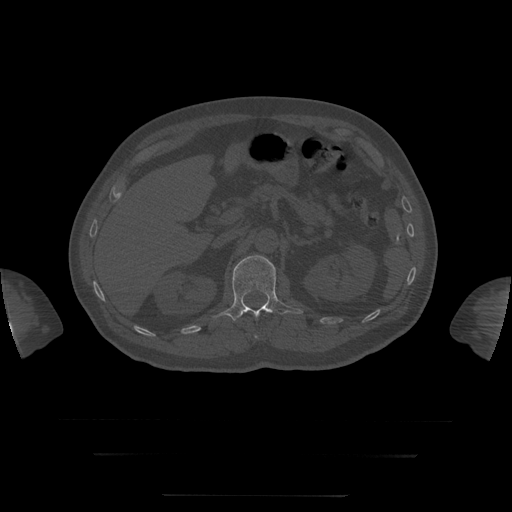
CT including the spine, one axial slice. Reconstruction kernel STANDARD. Bone window (W 1800 / L 400 HU). 1.25 mm slice thickness. 512 × 512 image matrix, field of view 510 × 510 mm. Patient age 73 years. Case-level facts recorded for this patient, not image findings: primary cancer: prostate.
Outlined on this slice (semi-automatic segmentation, software-assisted and operator-edited):
- L1 vertebra: bounding box [x1, y1, x2, y2] px = [213, 255, 303, 321]
- T12 vertebra: [255, 335, 258, 339]
- T8 vertebra: [238, 306, 272, 318]